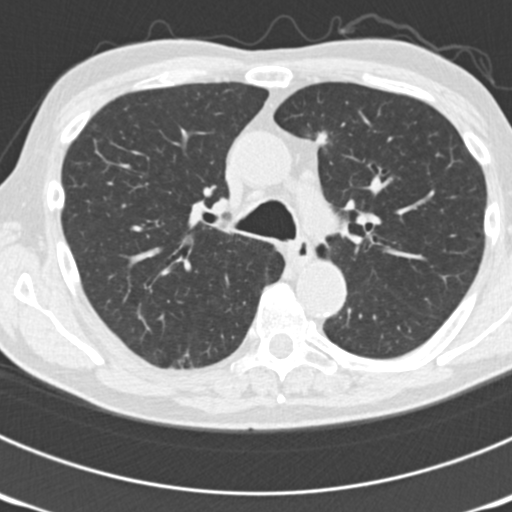
Low-dose screening chest CT, one axial slice; reconstruction kernel B30f; 120 kVp; lung window (W 1500 / L -600 HU); 2 mm slice thickness; 512 × 512 image matrix, field of view 300 × 300 mm.
Annotated regions visible in this slice (outlined manually by an expert reader):
- lesion 4 (tumor): bounding box (x1, y1, x2, y2) in pixels: (317, 131, 329, 146)